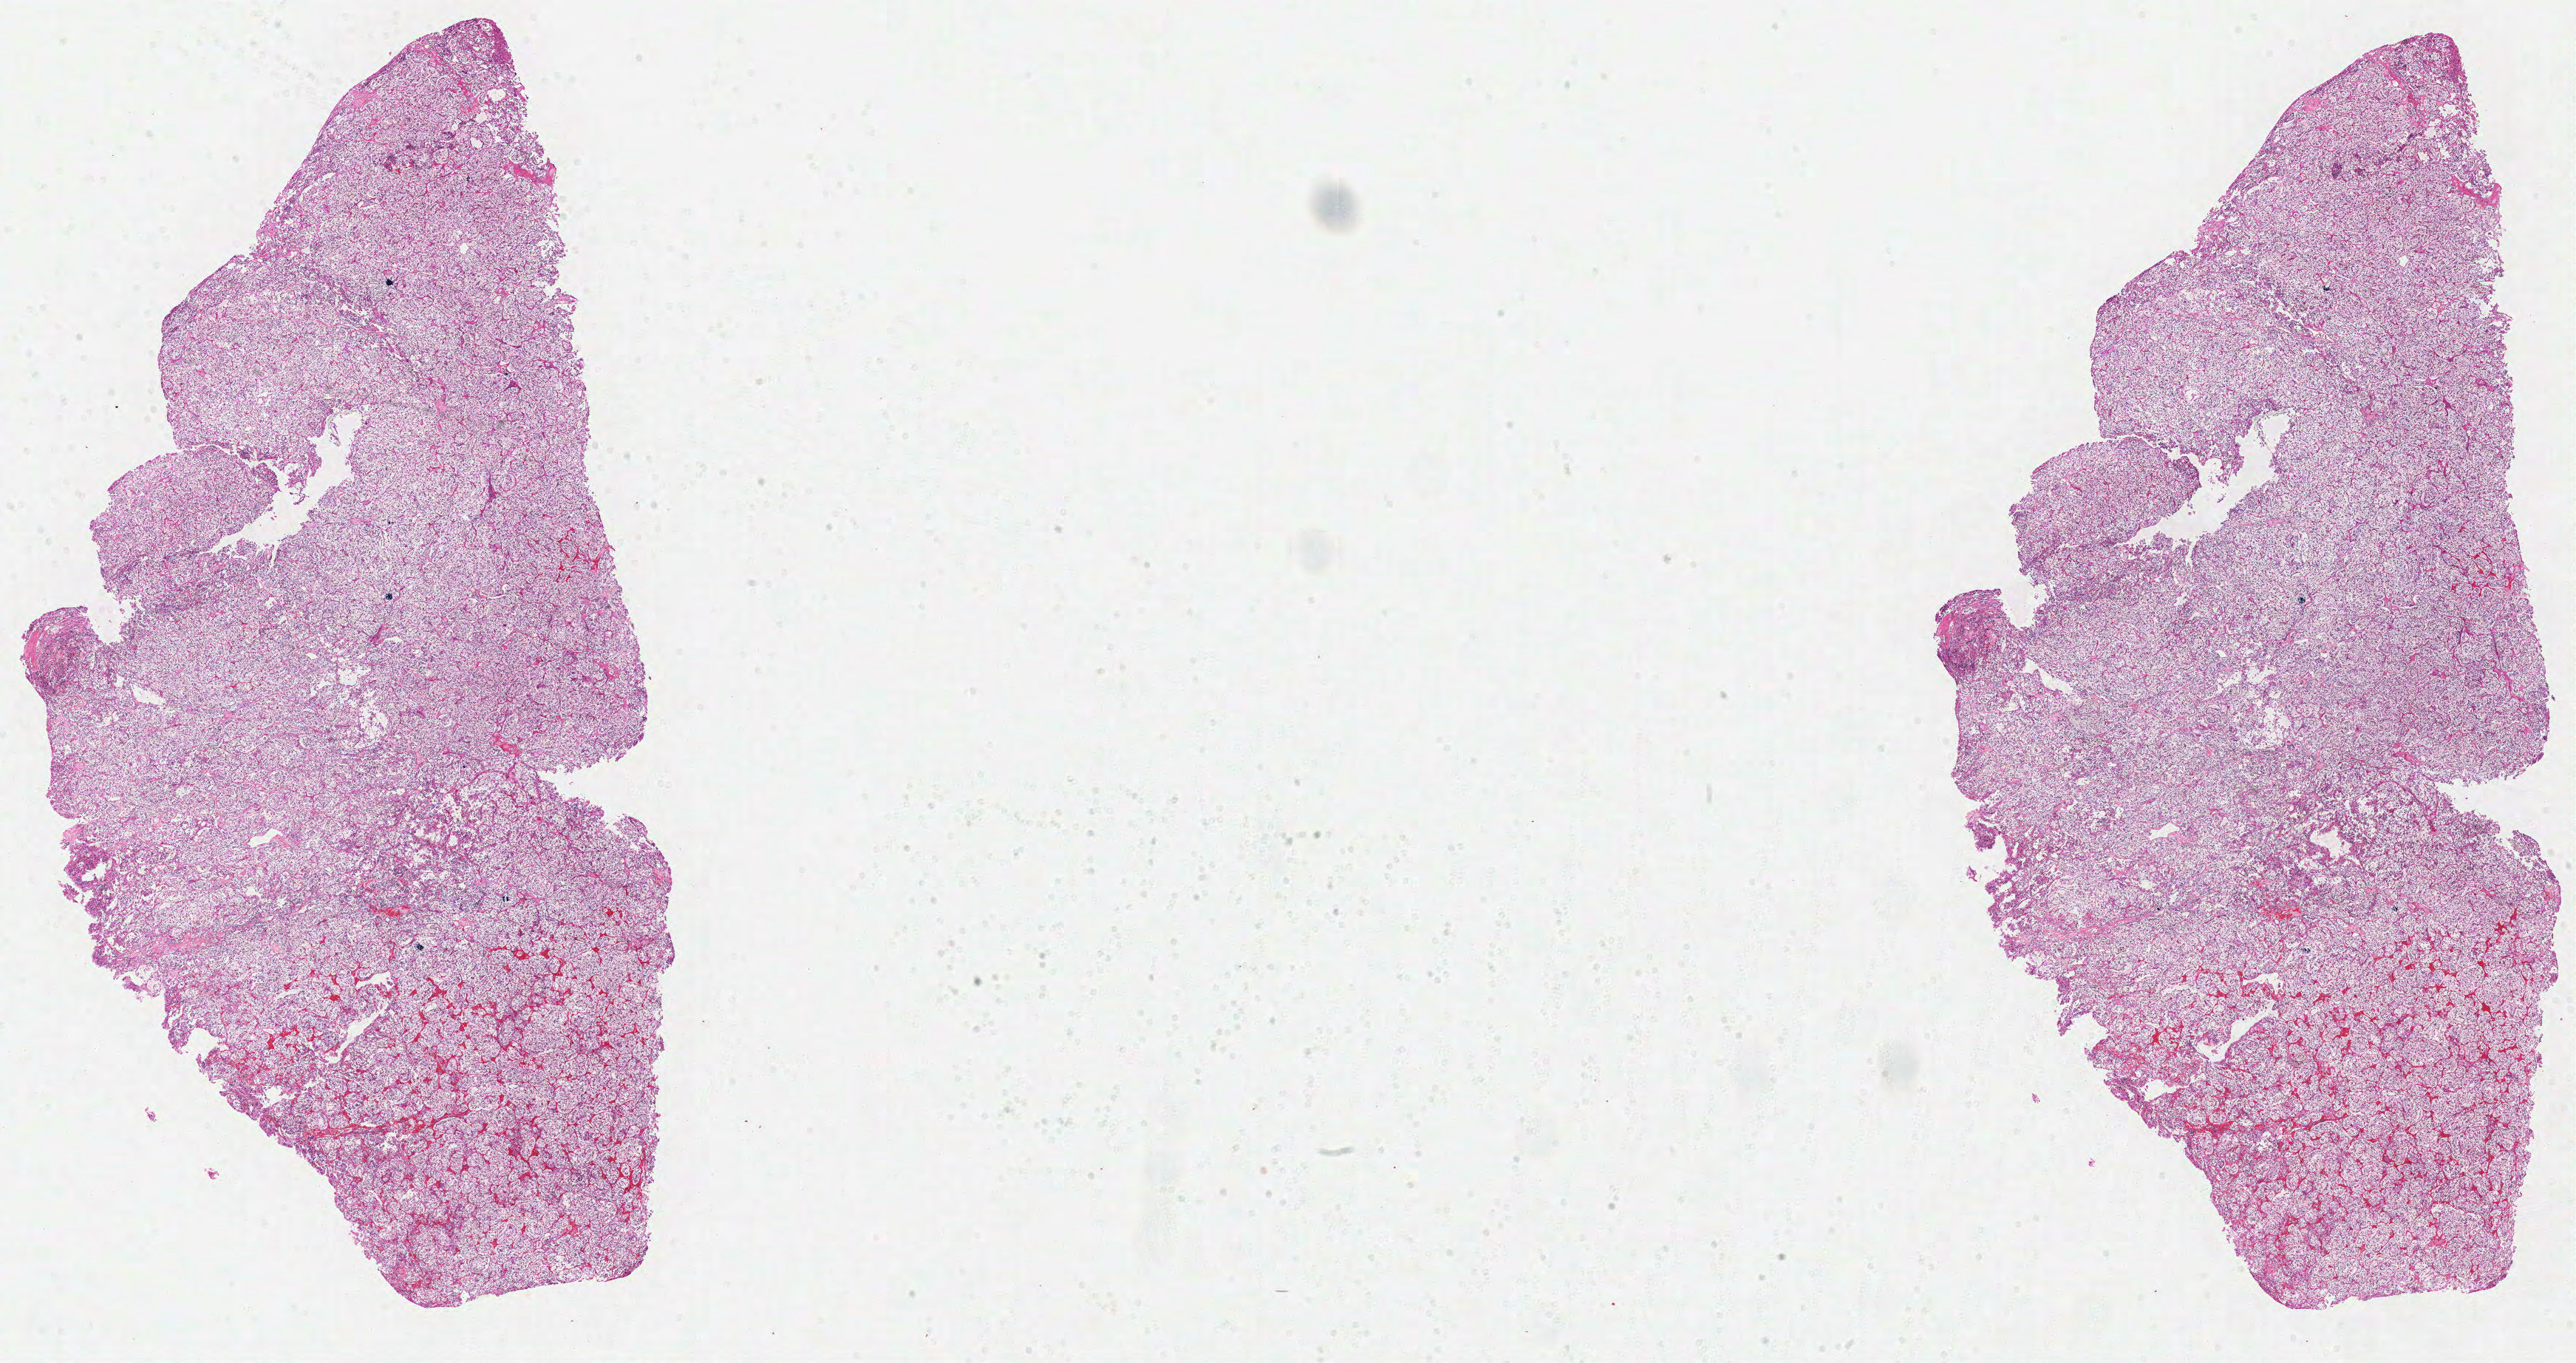
Hematoxylin and eosin (H&E) stained whole-slide image, whole scanned area (about 27.4 x 14.5 mm, acquisition: 40x scan) shown as a low-resolution overview. Formalin-fixed paraffin-embedded (FFPE) diagnostic section. Primary tumour sample from the kidney. Female patient; age at initial diagnosis 38 years. Histologic grade: G2 (moderately differentiated).
Histologic diagnosis: Clear cell adenocarcinoma, NOS. AJCC pathologic stage: I. Laterality: right.